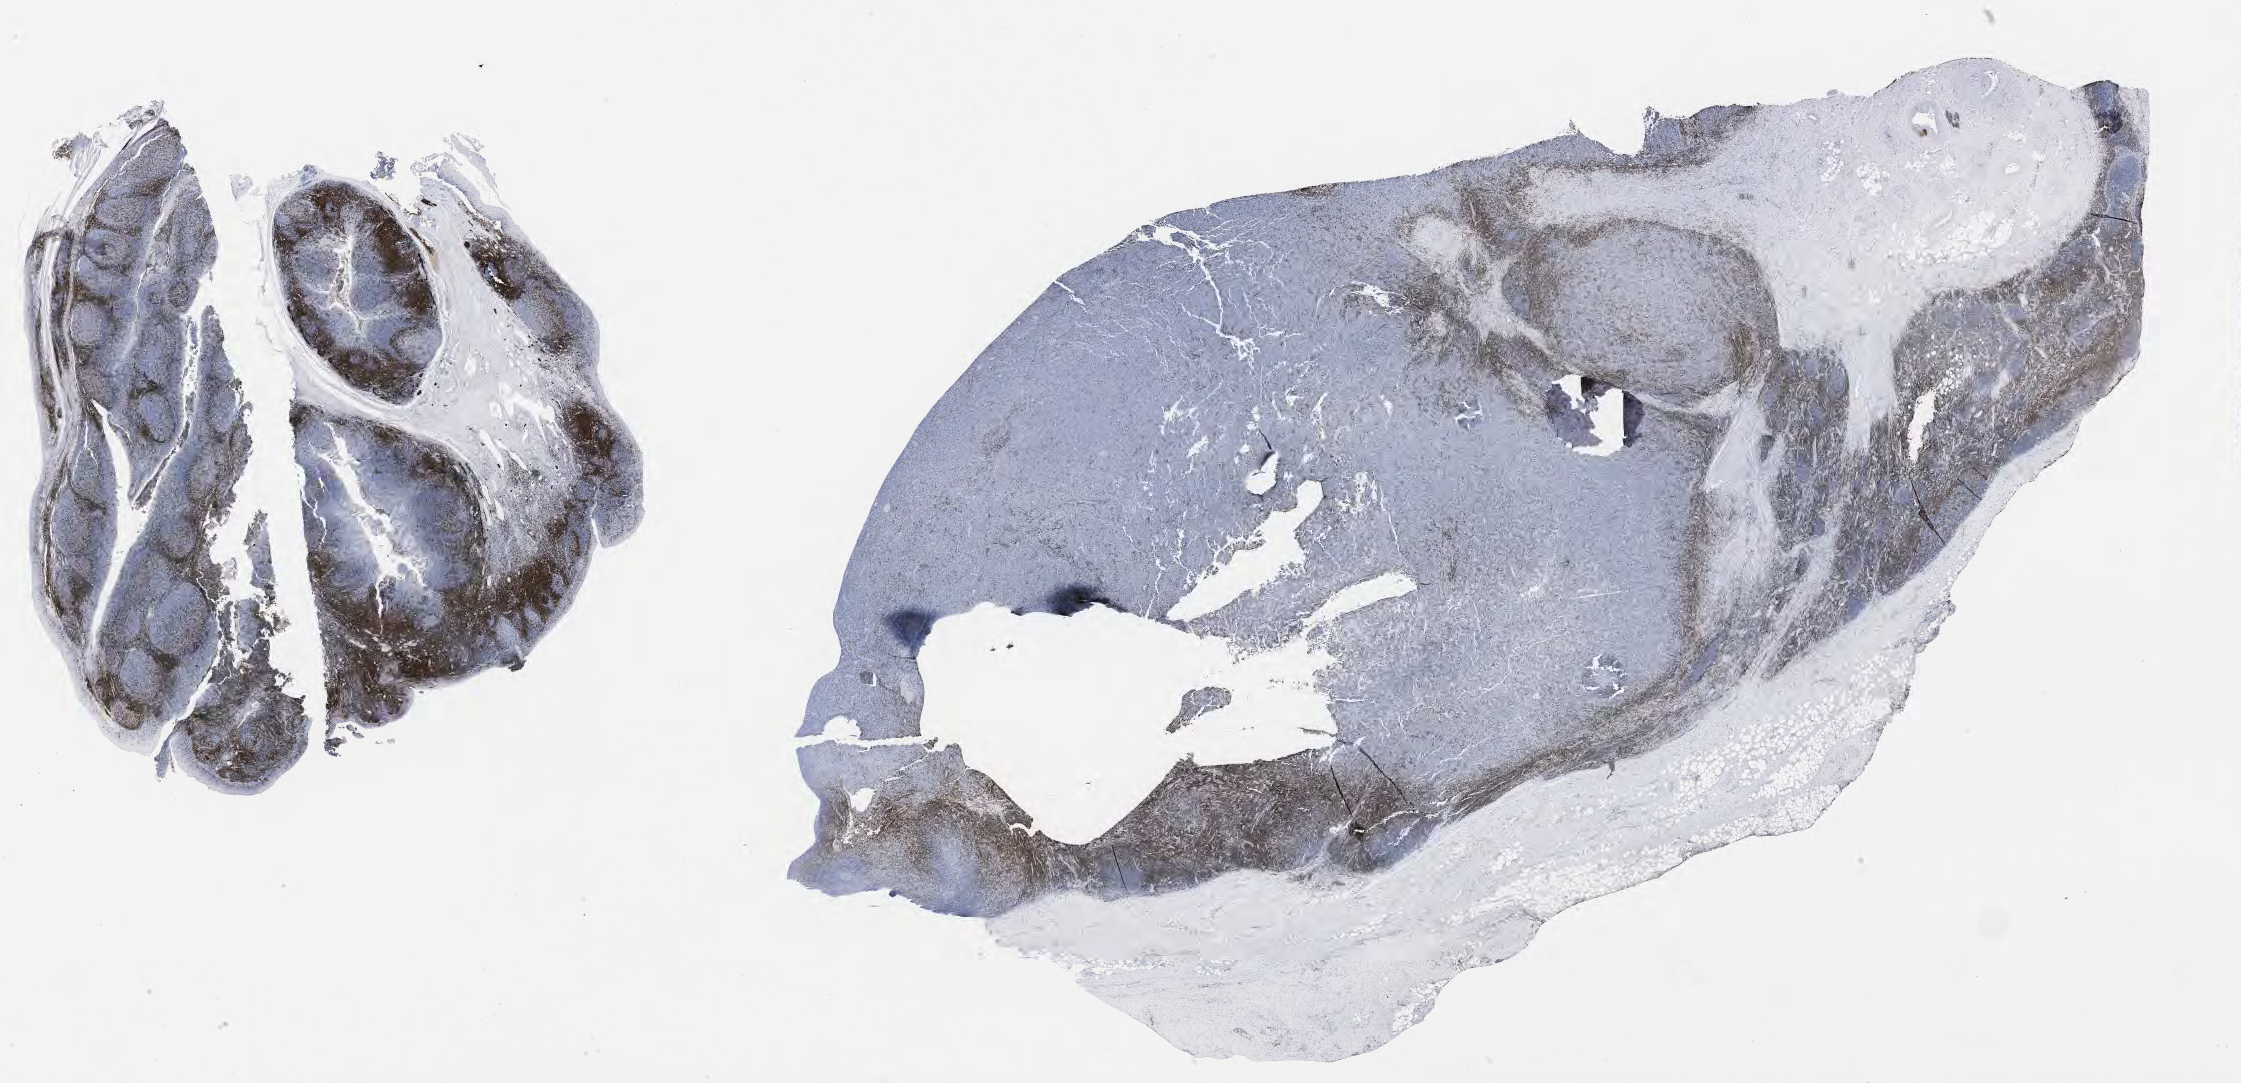
Immunohistochemistry (IHC) whole-slide image stained for CD3 — whole scanned area (about 36.2 x 17.5 mm) shown as a low-resolution overview, specimen: tumor tissue, anatomic site: lymph node. Patient: male, age 60 years.
Diagnosis: Diffuse large B-cell lymphoma, NOS.